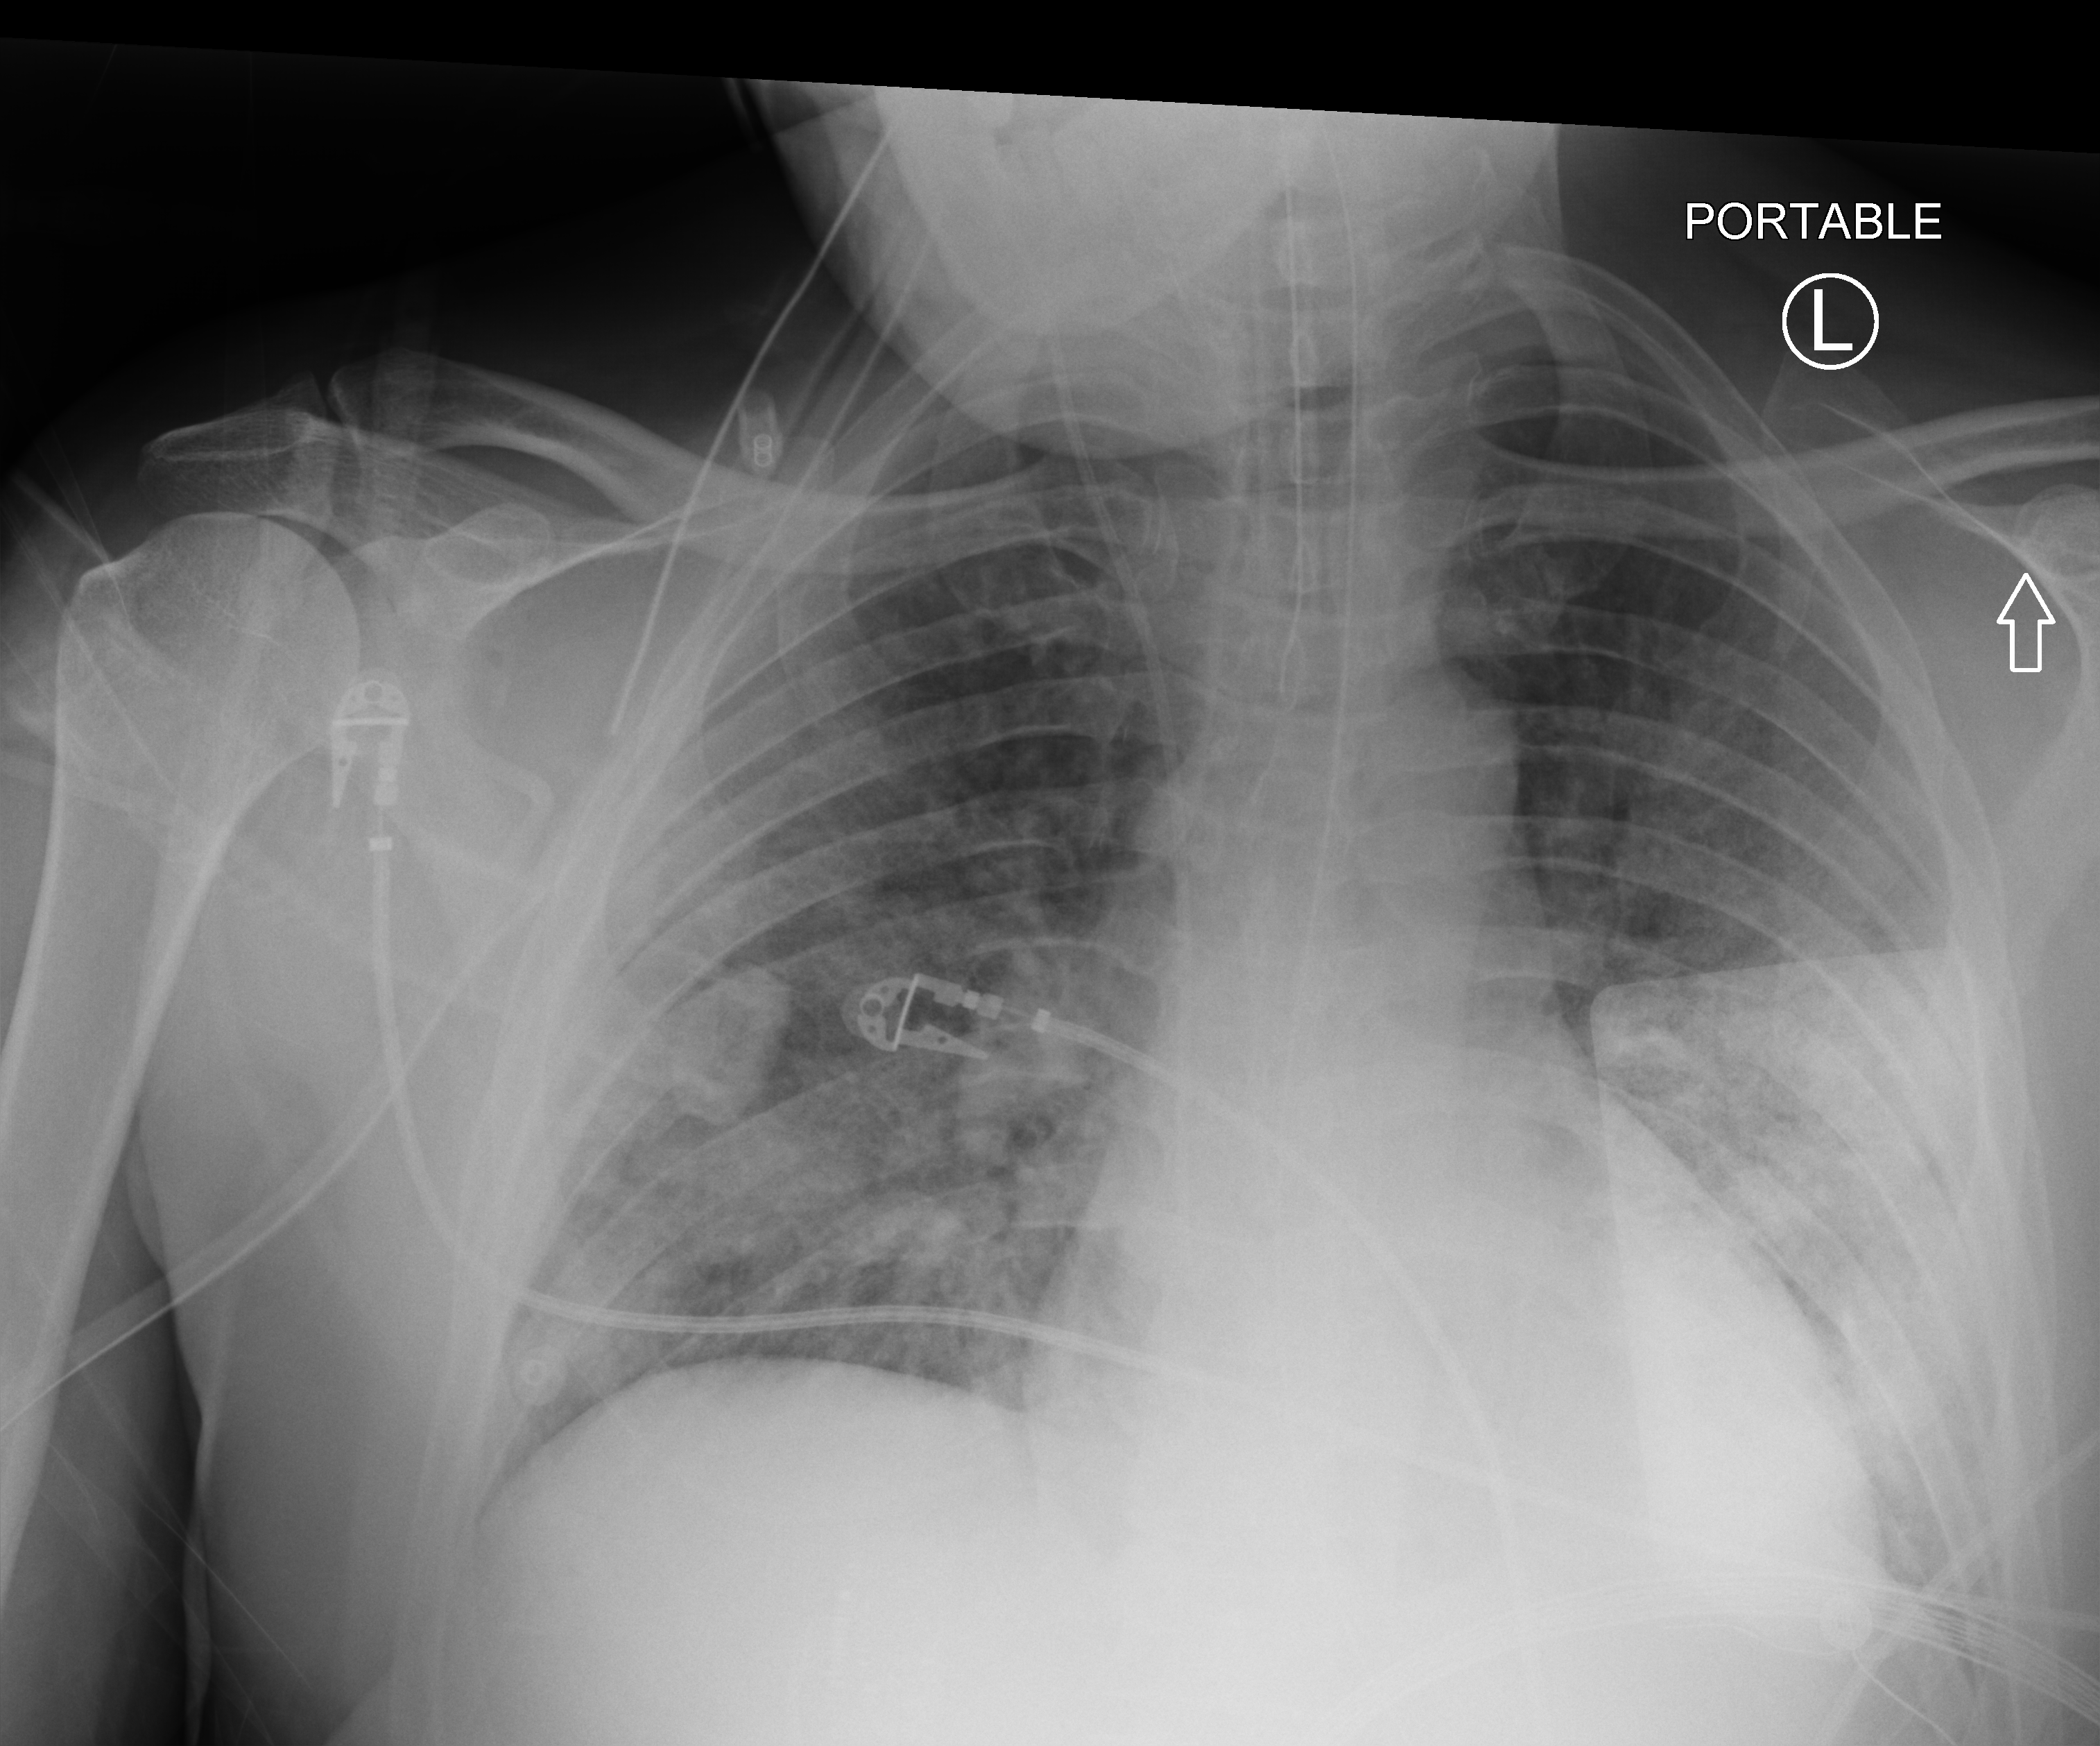
Chest X-ray (portable). Male patient hospitalised with COVID-19, age 18–59 years.
Admission-level facts for this patient (not findings on this image; timing relative to this image not recorded): admitted to intensive care during this hospital stay: yes.